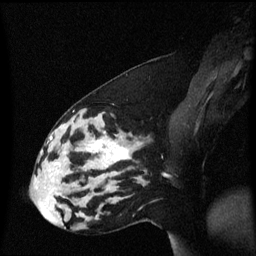
Breast MRI (dynamic contrast-enhanced), one sagittal slice; position 23 of 60 along the scan axis; dynamic contrast-enhanced series, image 2 of 3 at this slice position (ordered by acquisition); 1.5 T; TE 4.2 ms, TR 8.4 ms; 256 × 256 image matrix, field of view 210 × 210 mm. Female patient, age 33 years. Case-level facts recorded for this patient, not image findings: setting: breast cancer imaged before/during neoadjuvant chemotherapy; receptor status: triple-negative.
Annotated regions visible in this slice (semi-automatically segmented with operator editing):
- analysis volume of interest (the breast-tissue region the enhancement analysis was run in; not a lesion): bounding box (x1, y1, x2, y2) in pixels: (44, 123, 139, 189)
- tumour enhancement mask (voxels above the 70 % enhancement threshold inside the analysis volume of interest): (88, 138, 131, 167)